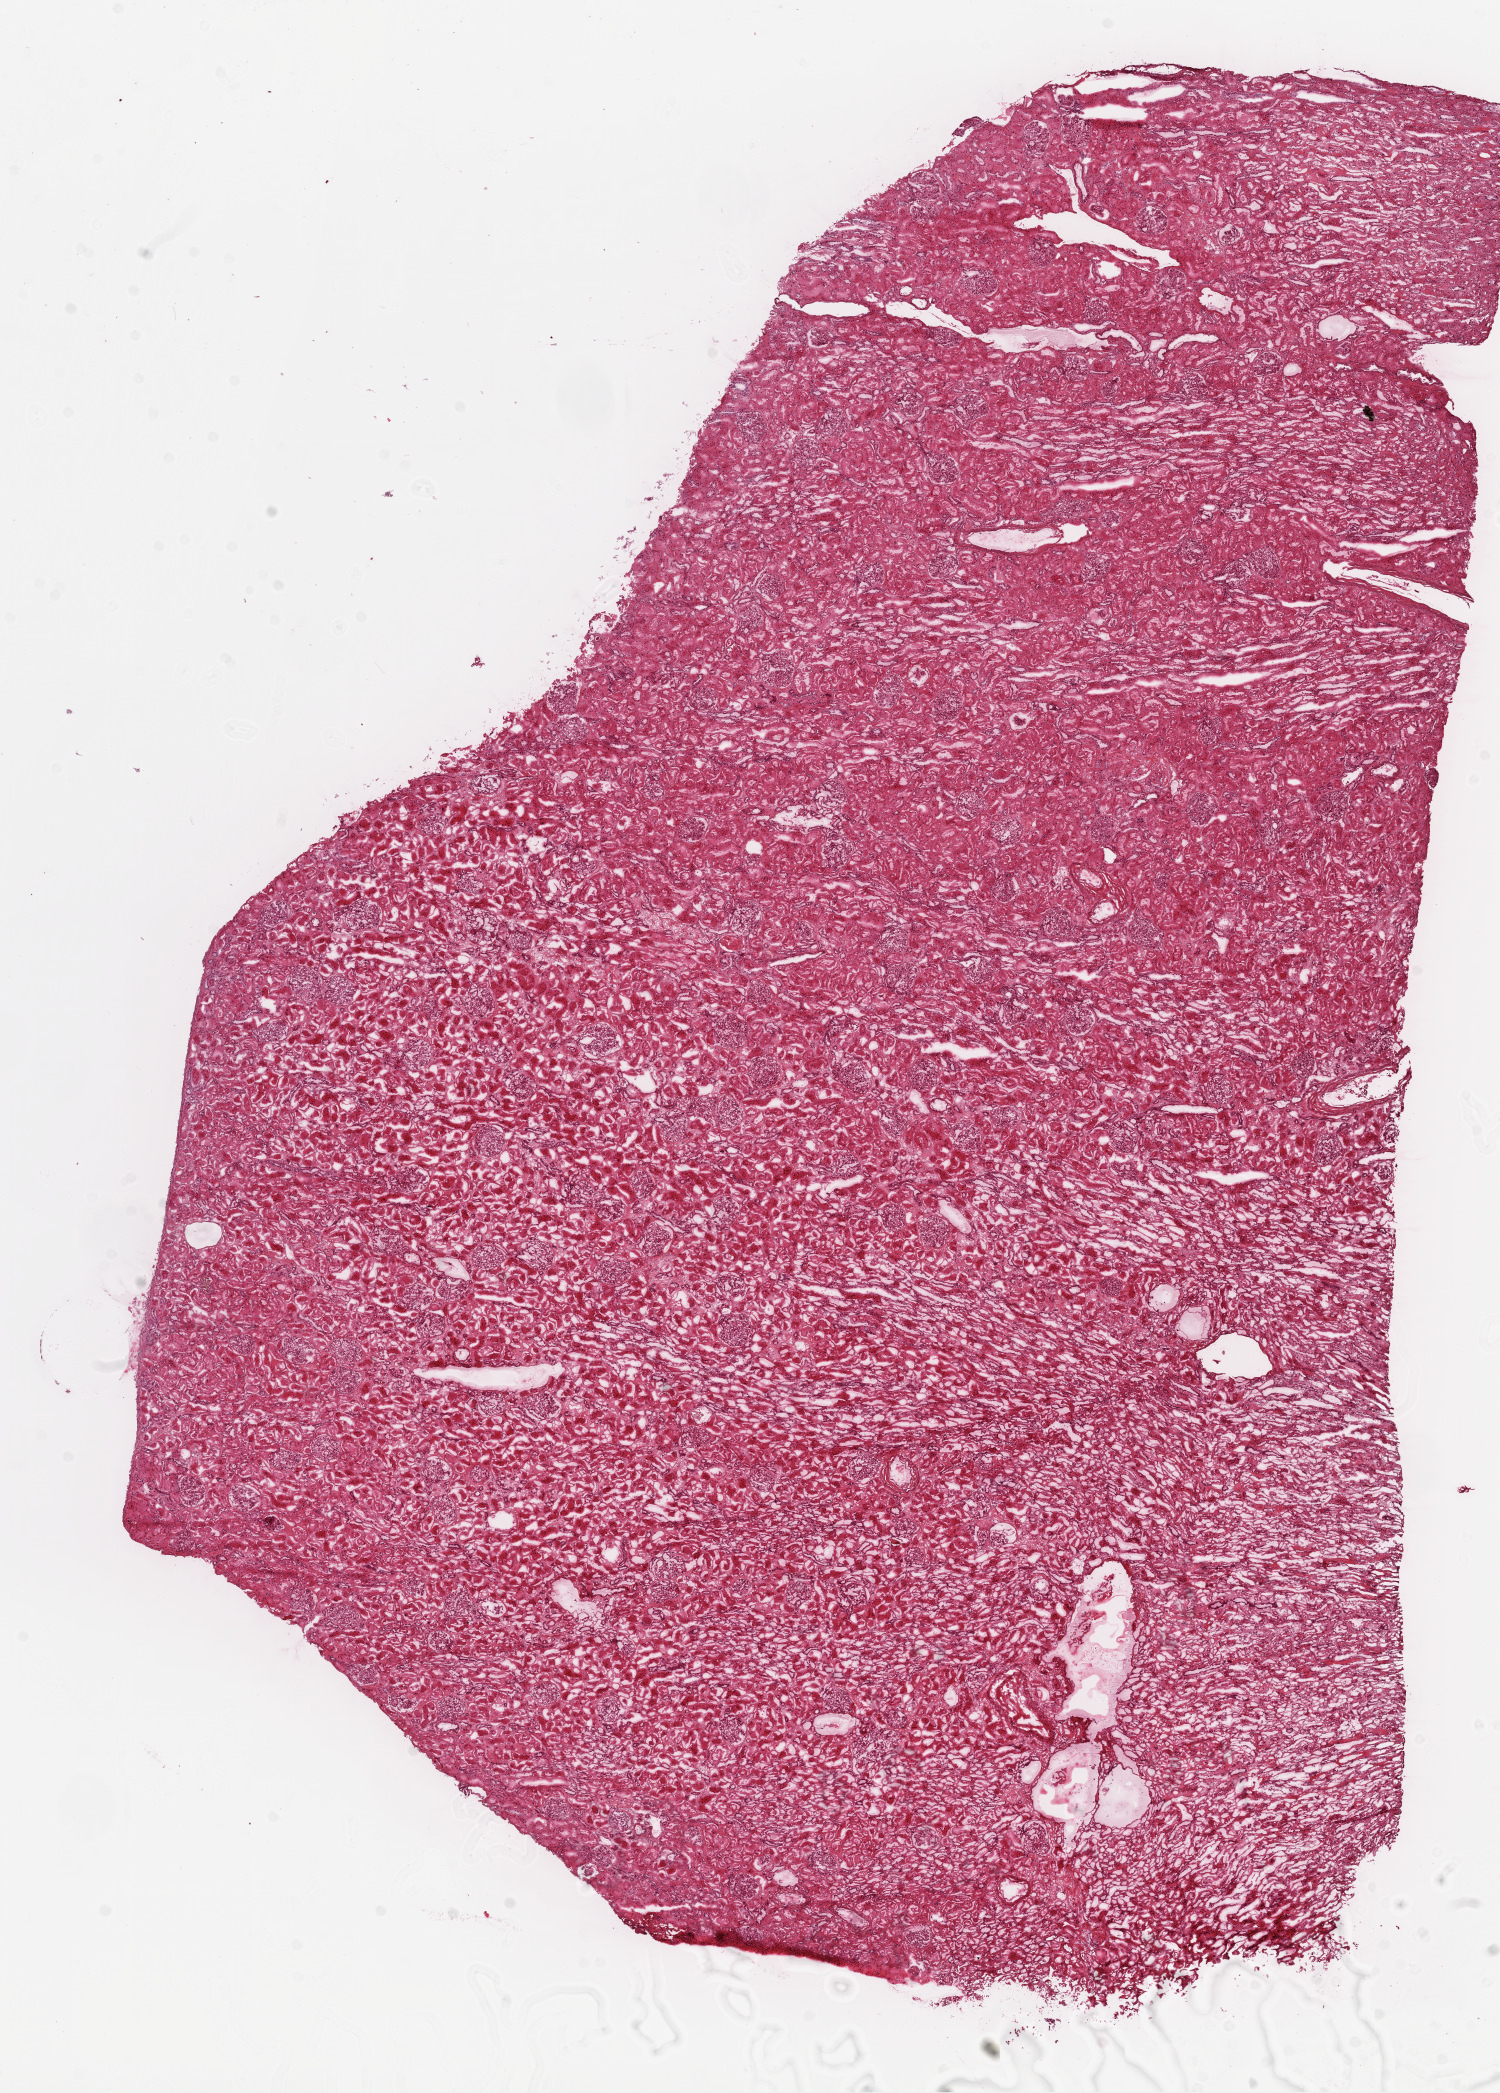
Whole-slide histology image, H&E-stained, shown as a low-resolution overview of the whole scanned area (about 12.0 x 16.8 mm), frozen section from the top of the tissue portion, sample: solid tissue normal (non-tumour tissue), kidney. Male, age 58 years at initial diagnosis.
This section: solid tissue normal sample (biorepository sample class). Patient diagnosis: Clear cell adenocarcinoma, NOS.